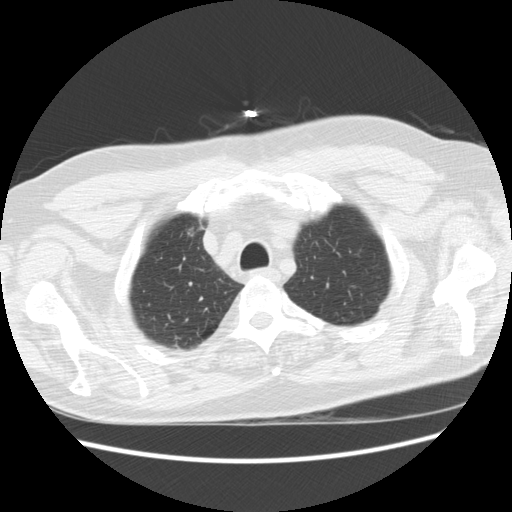
Low-dose screening chest CT, axial slice, first (baseline) screen, lung window (W 1500 / L -600 HU), 2.5 mm slice thickness. Male participant, aged 66 years at enrolment.
• Lesion marked by an expert reader, bounding box [x1, y1, x2, y2] px = [174, 212, 210, 251].
• No non-calcified nodule or mass ≥4 mm was recorded by the screening reader at this exam.
• Official screen result: negative screen, significant abnormalities not suspicious for lung cancer.
• Later outcome: lung cancer diagnosed 951 days after this screen (after the third annual screen) — bronchiolo-alveolar adenocarcinoma, NOS, right upper lobe, moderately differentiated (G2), stage IA (AJCC 6th edition), 12 mm at pathology.